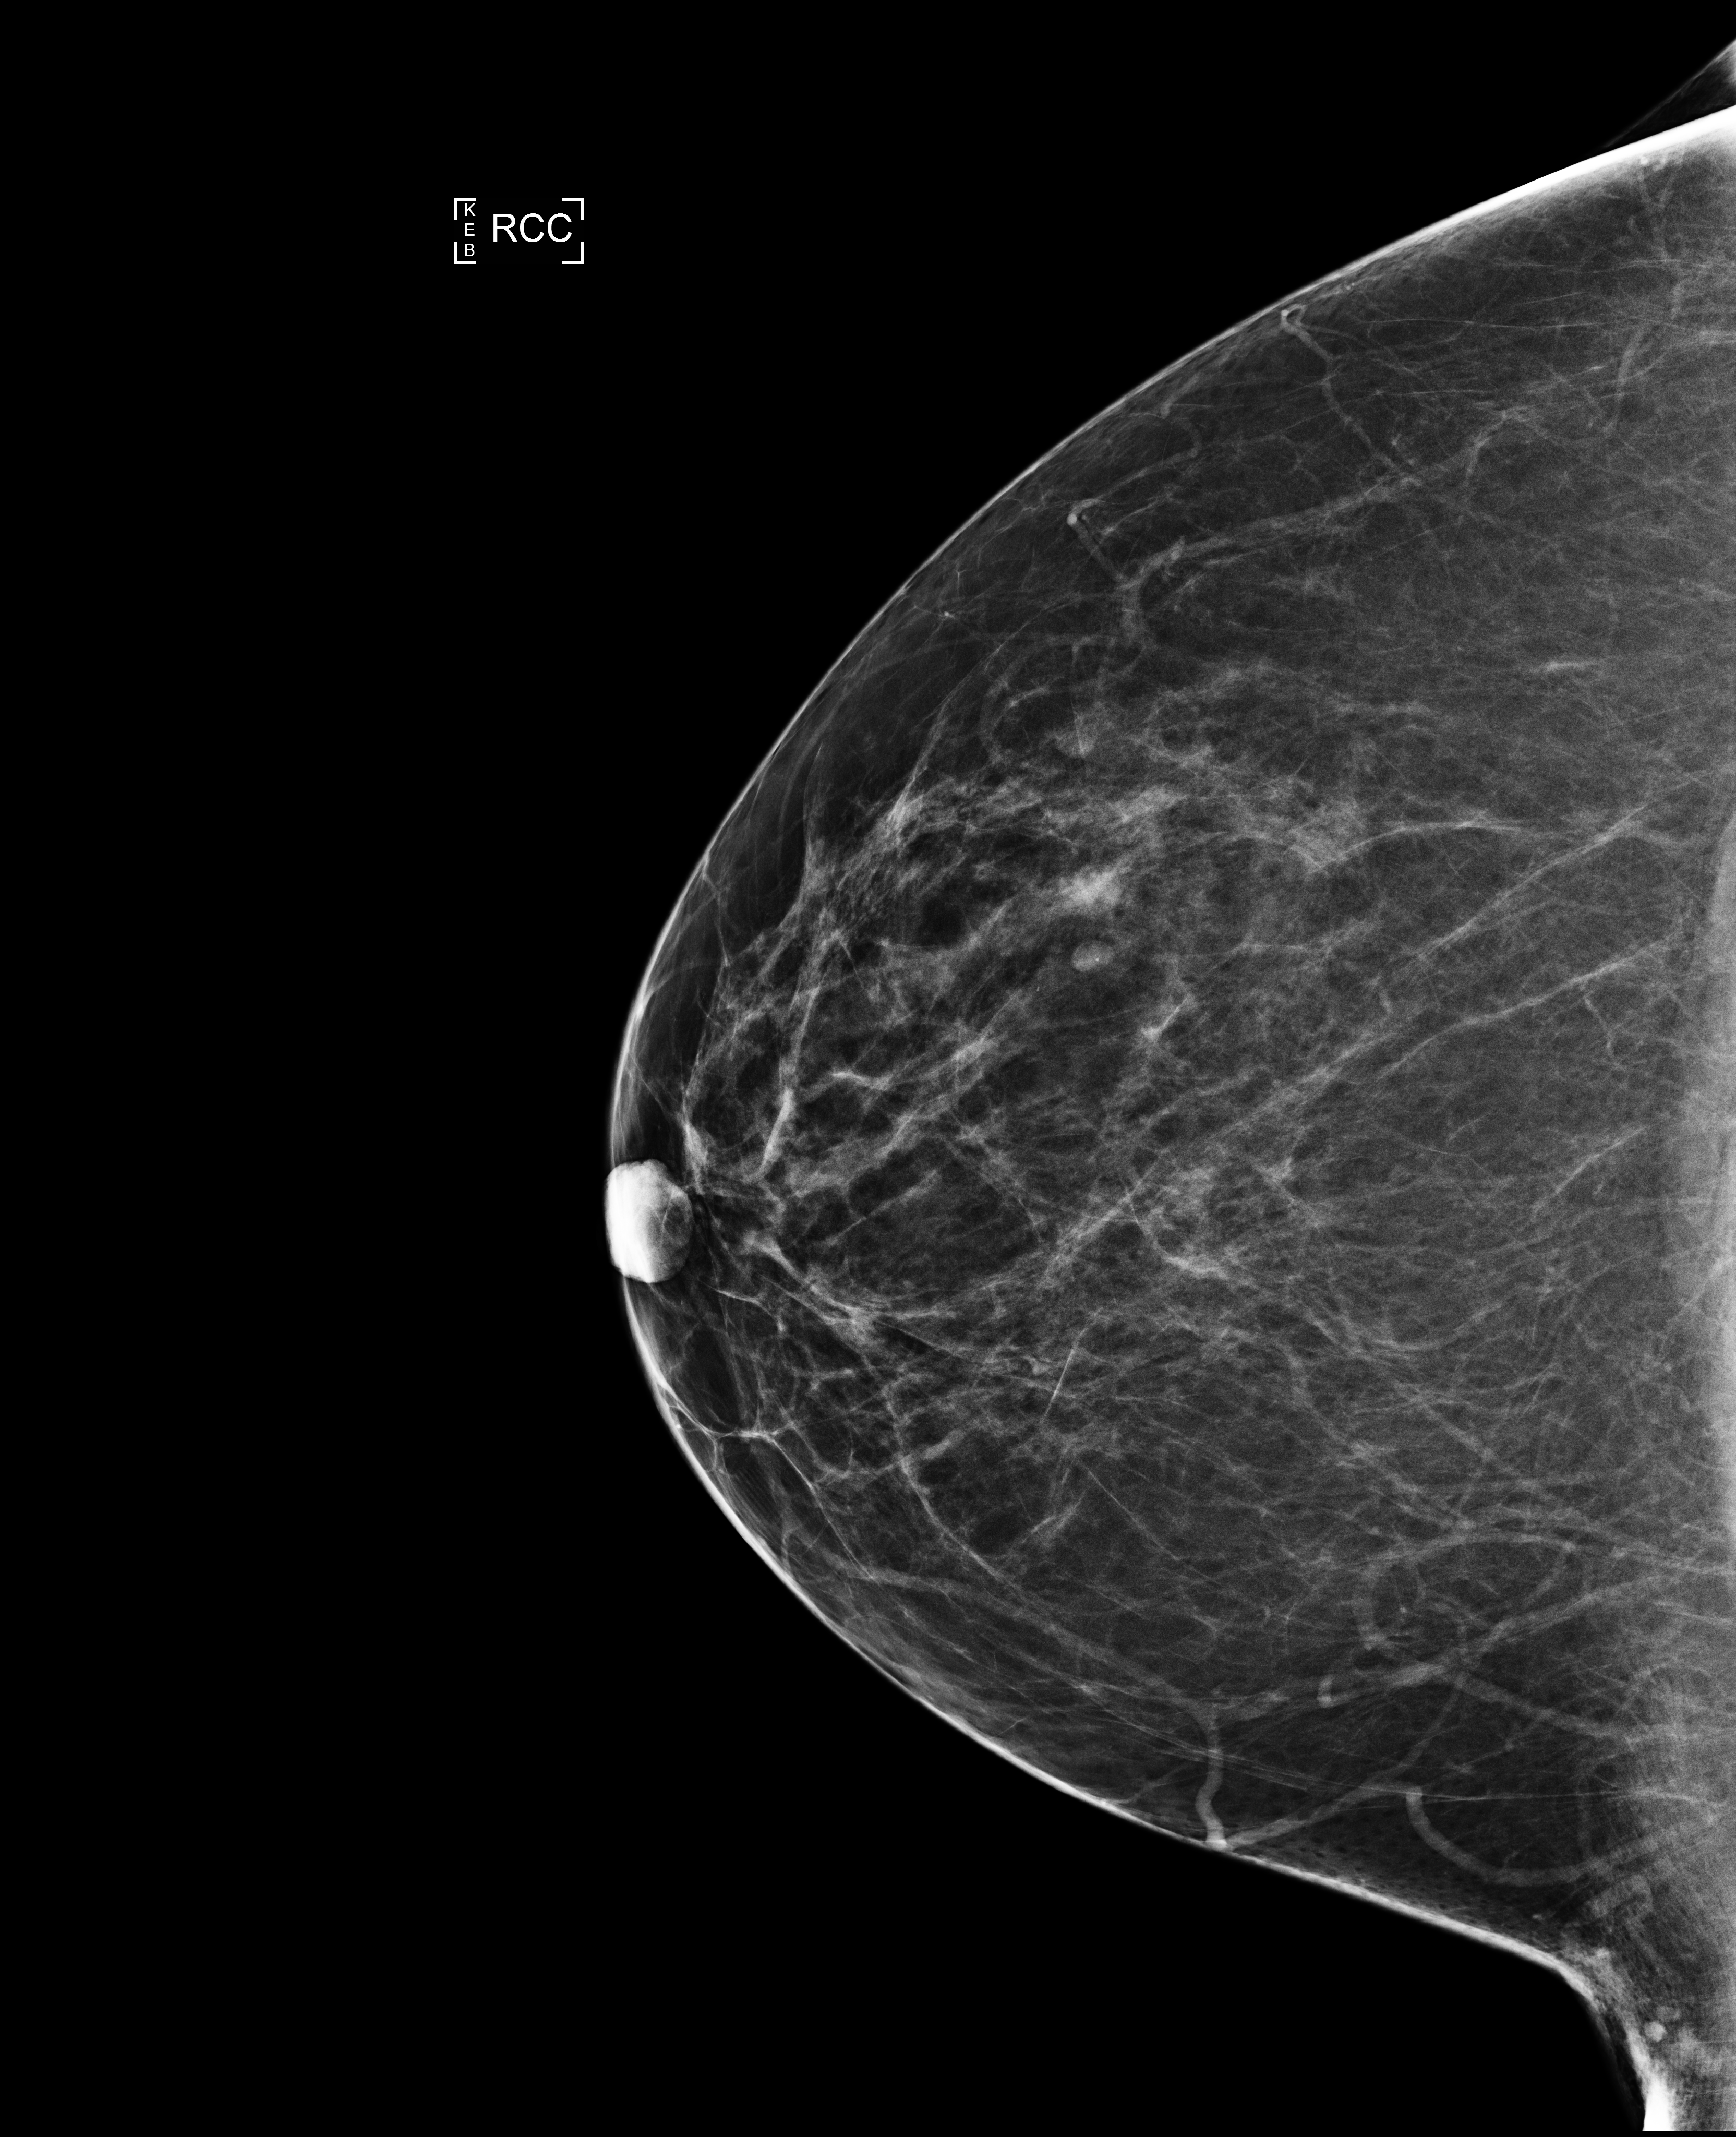
Screening examination; compressed breast thickness 69 mm. Patient aged 53 years (female).
Image type: full-field digital mammogram. Breast: right. Projection: cranio-caudal projection.